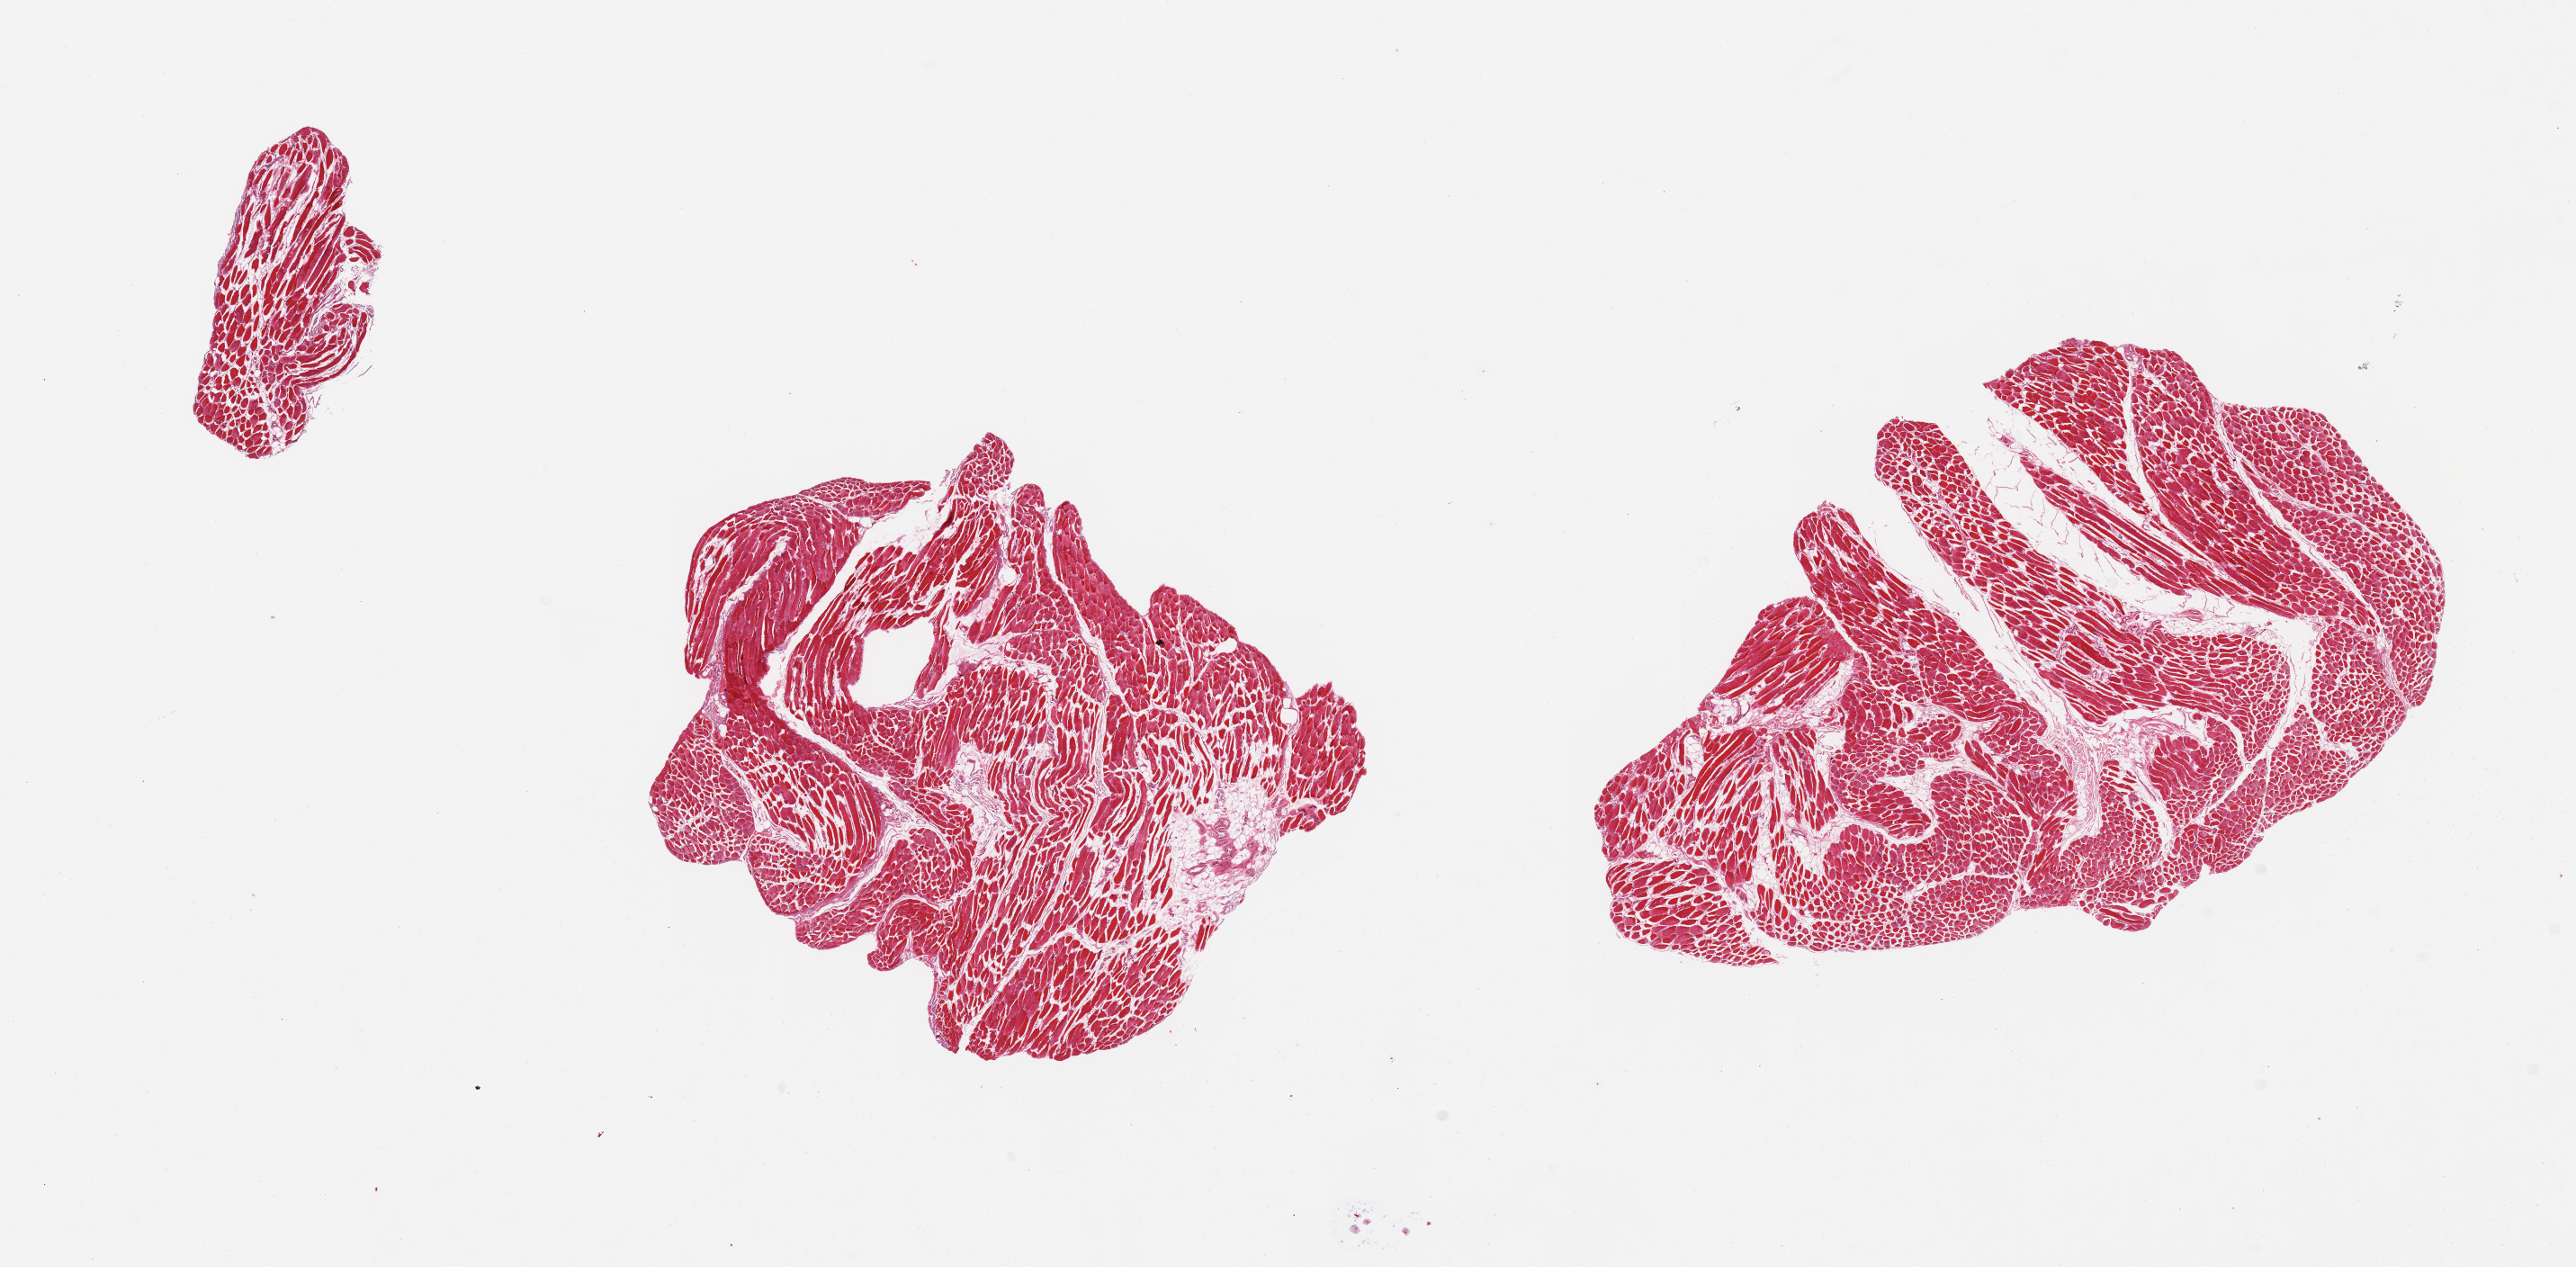
Whole-slide image, H&E stain, low-resolution overview of the scanned area, about 22.6 x 11.1 mm, PAXgene-fixed, paraffin-embedded tissue, section of skeletal muscle (target tissue), donor tissue sample. Donor: male.
- reviewer comment on this tissue sample: 3 pieces; no fat